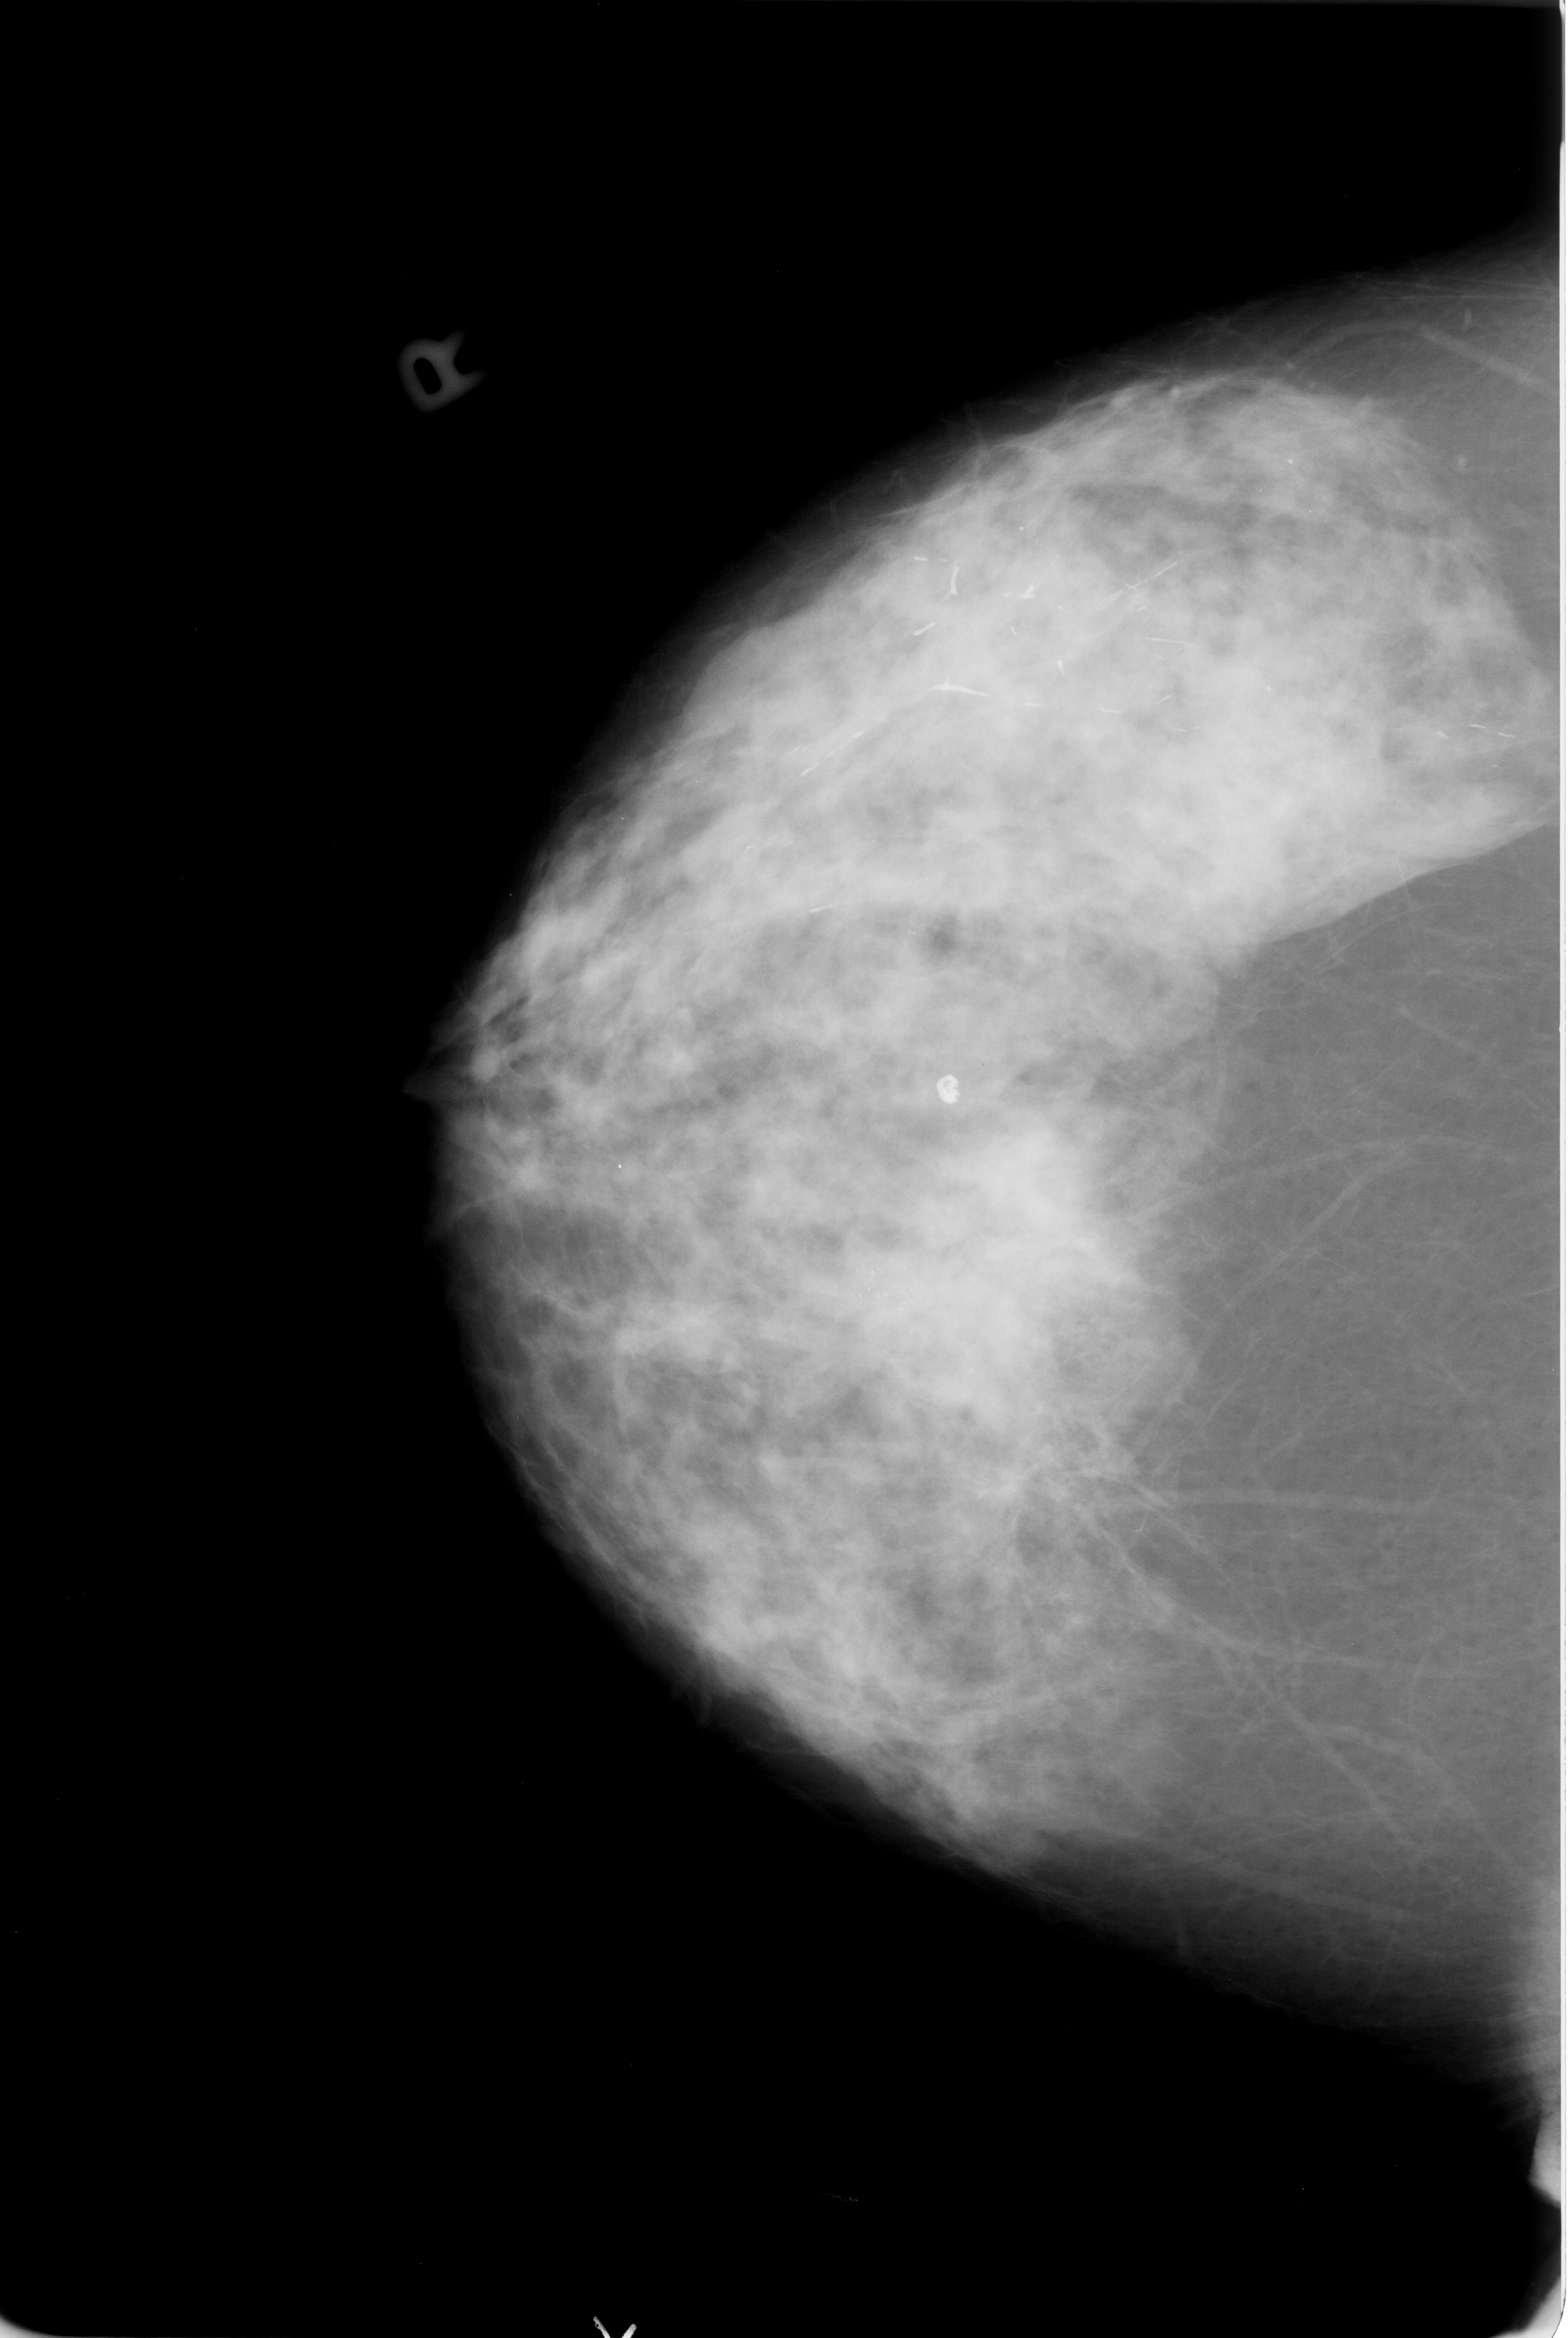
Scanned film-screen mammogram, right breast, CC view, breast composition: heterogeneously dense (BI-RADS density category 3 of 4).
Abnormality record for this image: Finding 1 of 3: calcifications, morphology pleomorphic, distribution clustered; BI-RADS assessment category 4; subtlety rating 3 on a 1 (subtle) to 5 (obvious) scale; pathology (as recorded): malignant. Finding 2 of 3: calcifications, morphology pleomorphic, distribution clustered; BI-RADS assessment category 4; subtlety rating 3 on a 1 (subtle) to 5 (obvious) scale; pathology (as recorded): malignant. Finding 3 of 3: calcifications, morphology pleomorphic, distribution clustered; BI-RADS assessment category 4; pathology (as recorded): malignant.